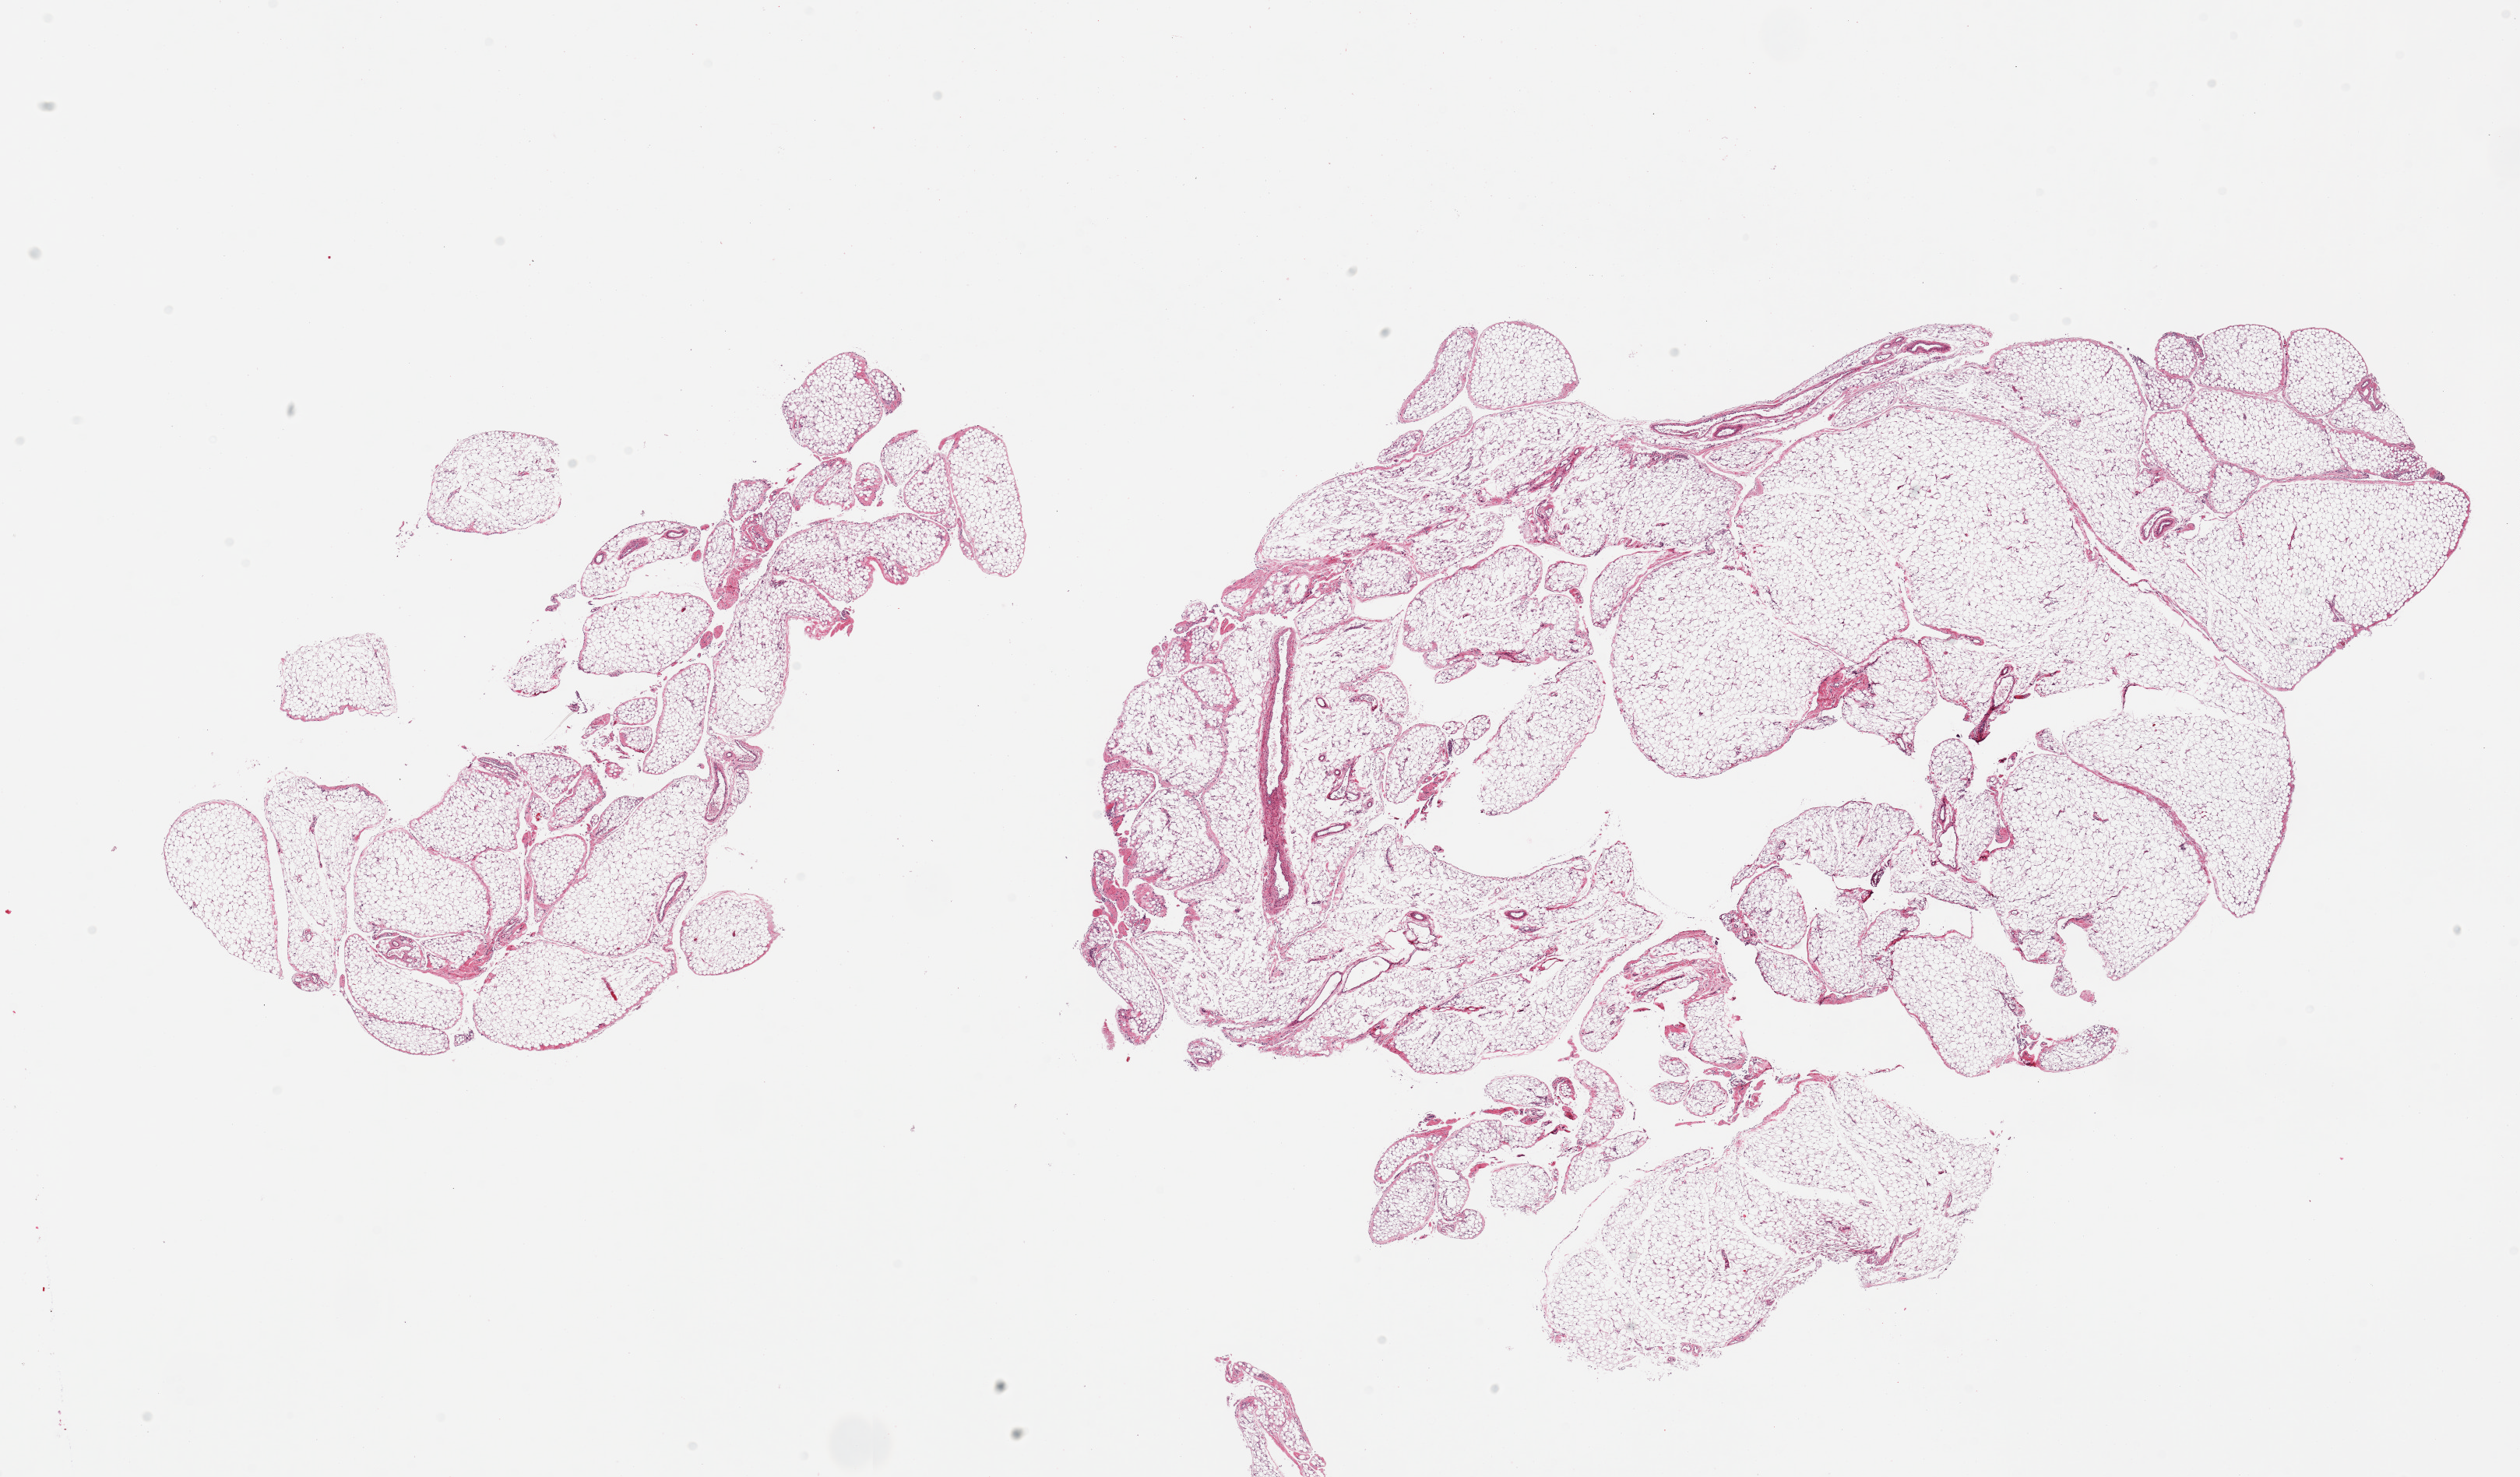
H&E whole-slide image, brightfield — a low-resolution overview of the entire scanned area, about 25.6 x 15.0 mm (acquisition: 20x scan). PAXgene-fixed, paraffin-embedded tissue. Target tissue: omentum. Donor tissue sample.
Reviewer comment on this tissue sample: 2 pieces.